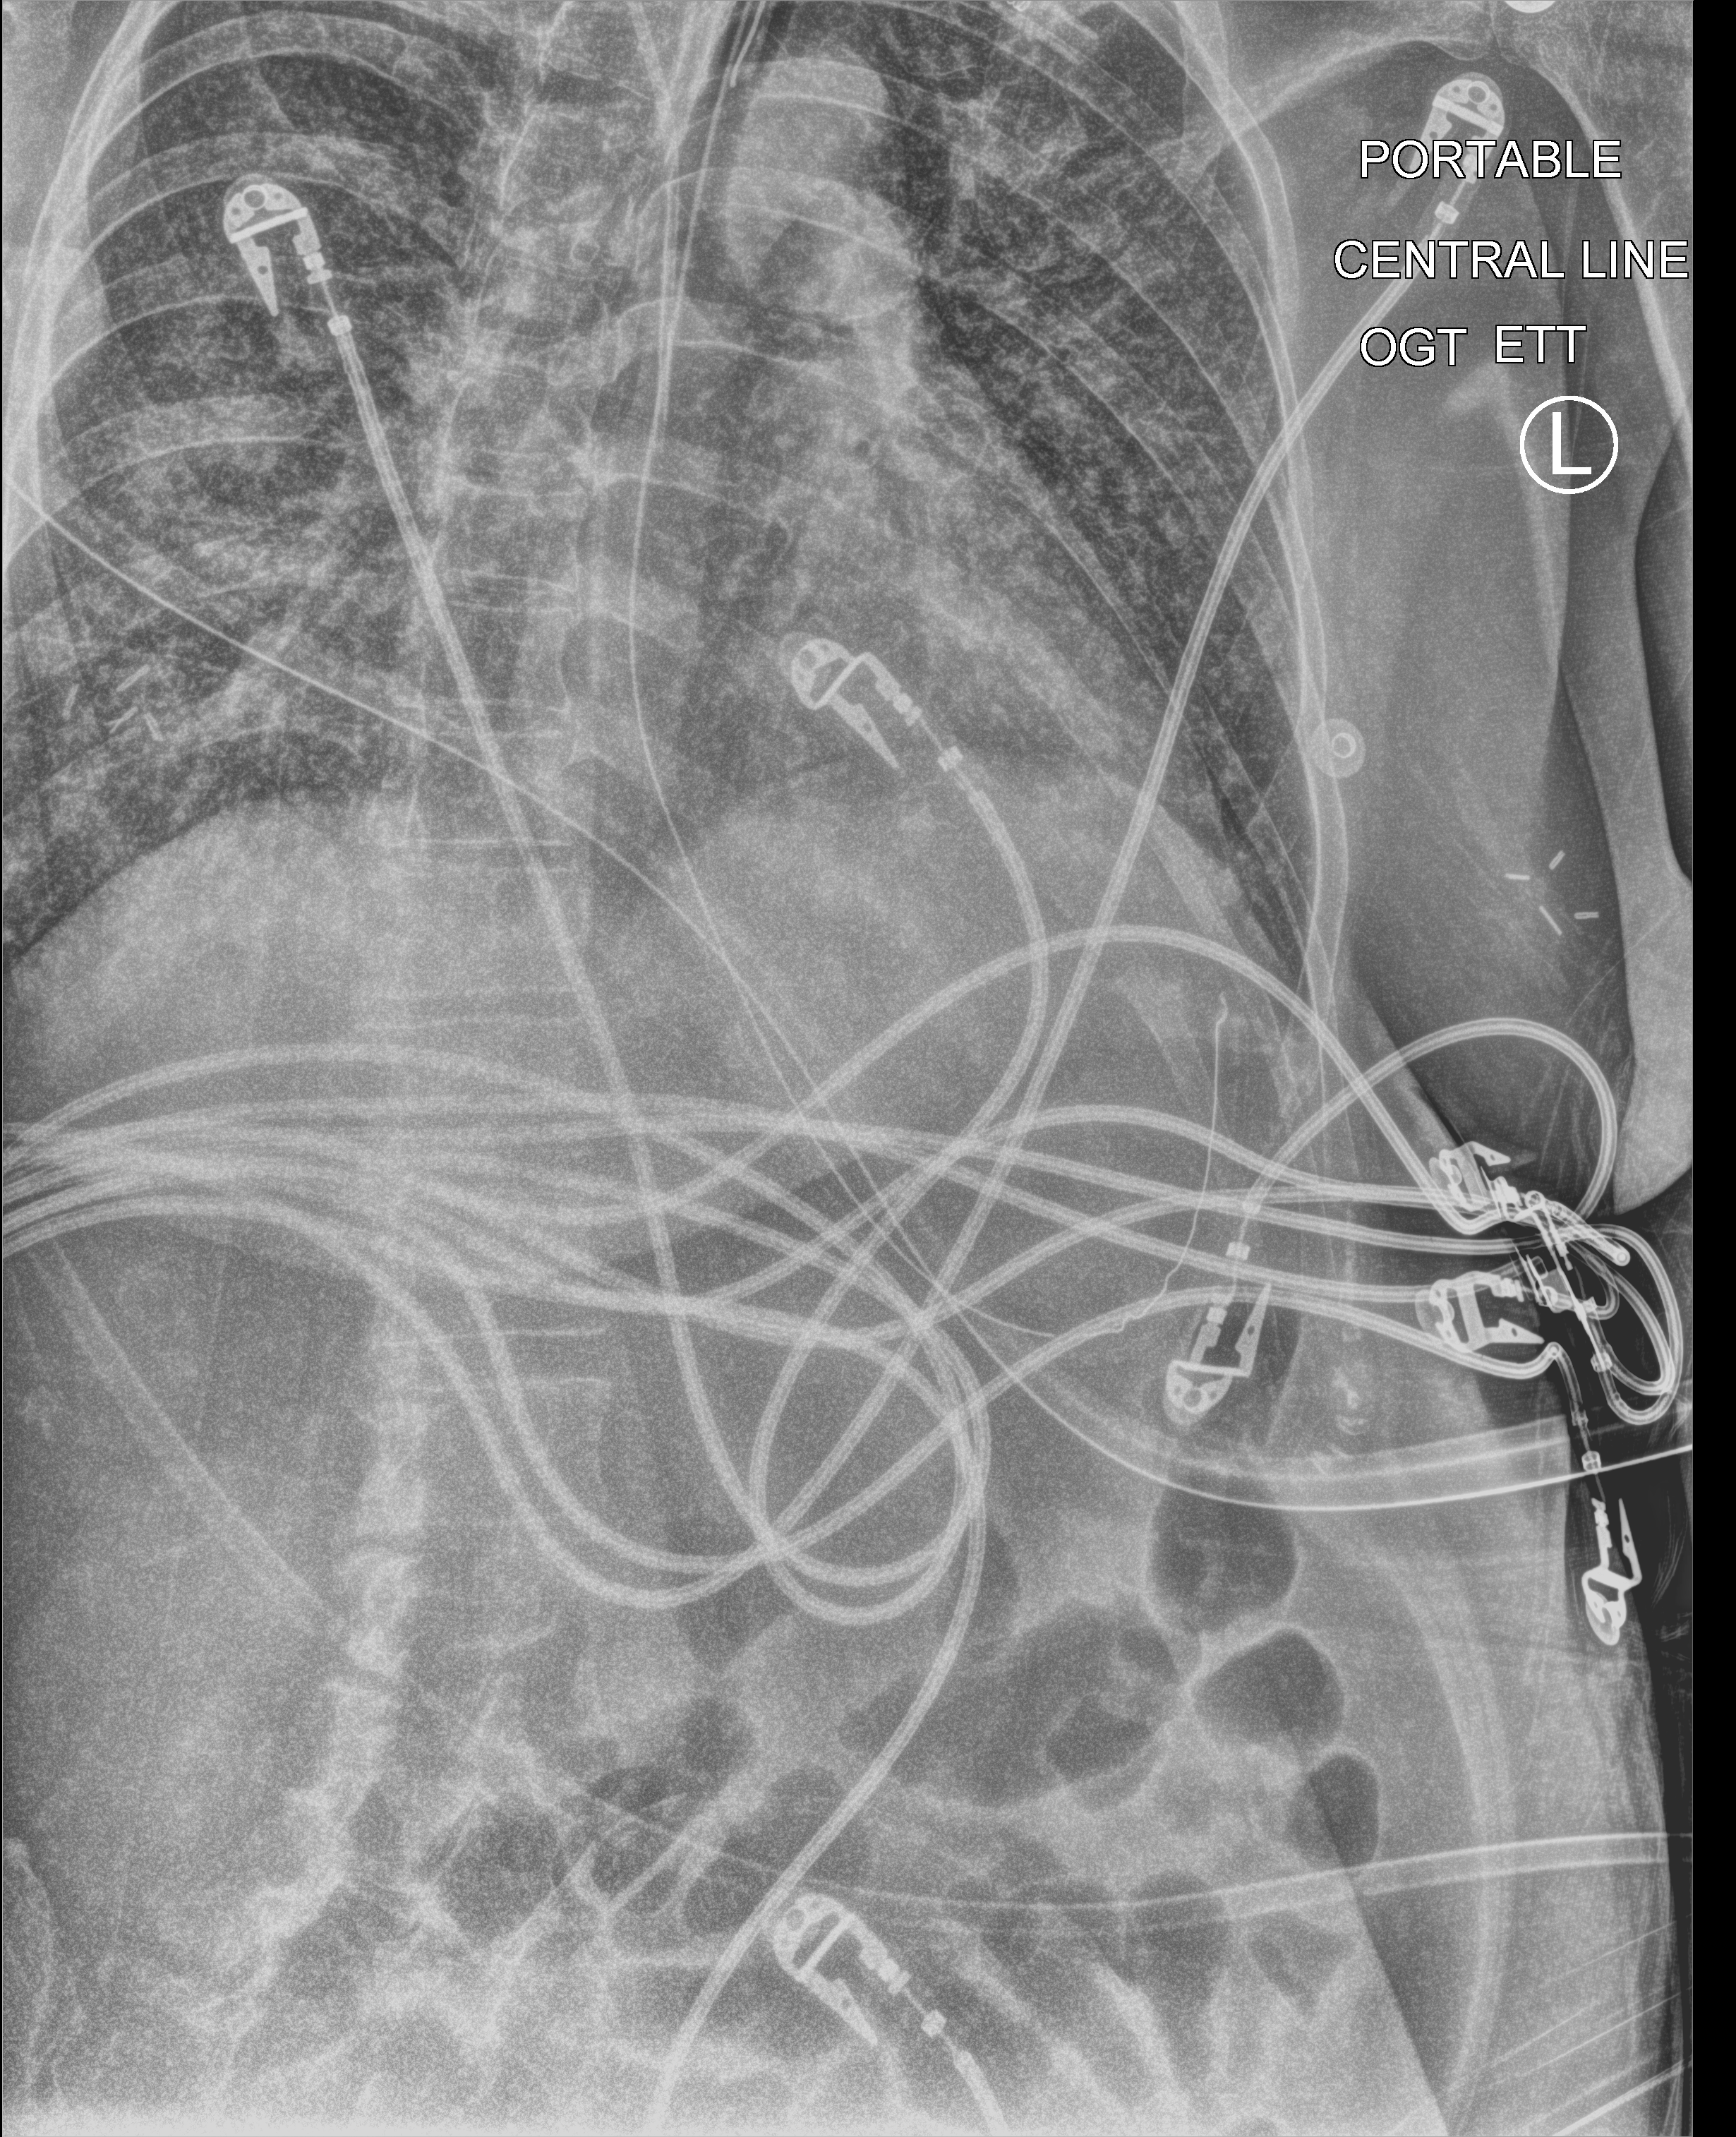
Chest X-ray (portable); anteroposterior (AP) projection. Female patient hospitalised with COVID-19, age 18–59 years.
Hospital-stay facts (about this admission, not read from this image; timing relative to this image not recorded):
- length of hospital stay: 21 days
- chronic kidney disease (admission record): no